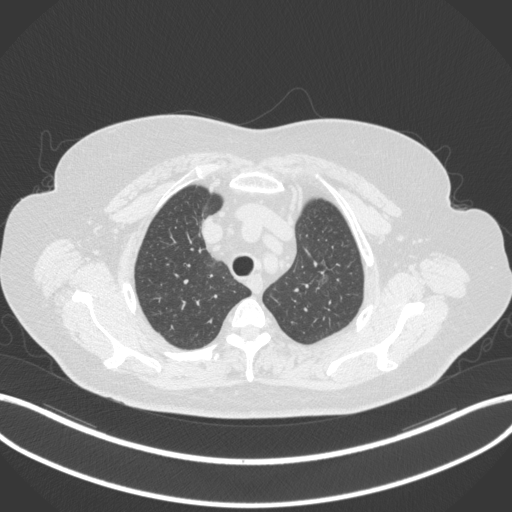
Chest CT, one axial slice. Slice 275 of 310 in the series (ordered by position). 120 kVp. Lung window (W 1500 / L -600 HU). 1 mm slice thickness. 512 × 512 image matrix, field of view 400 × 400 mm. Female patient, age 70 years. Case-level facts recorded for this patient, not image findings: clinical TNM (as recorded): T1c N0 M0.
Annotated regions visible in this slice (bounding box drawn by a radiologist):
- lung tumour (recorded histology: adenocarcinoma): bounding box [x1, y1, x2, y2] px = [311, 262, 331, 293]